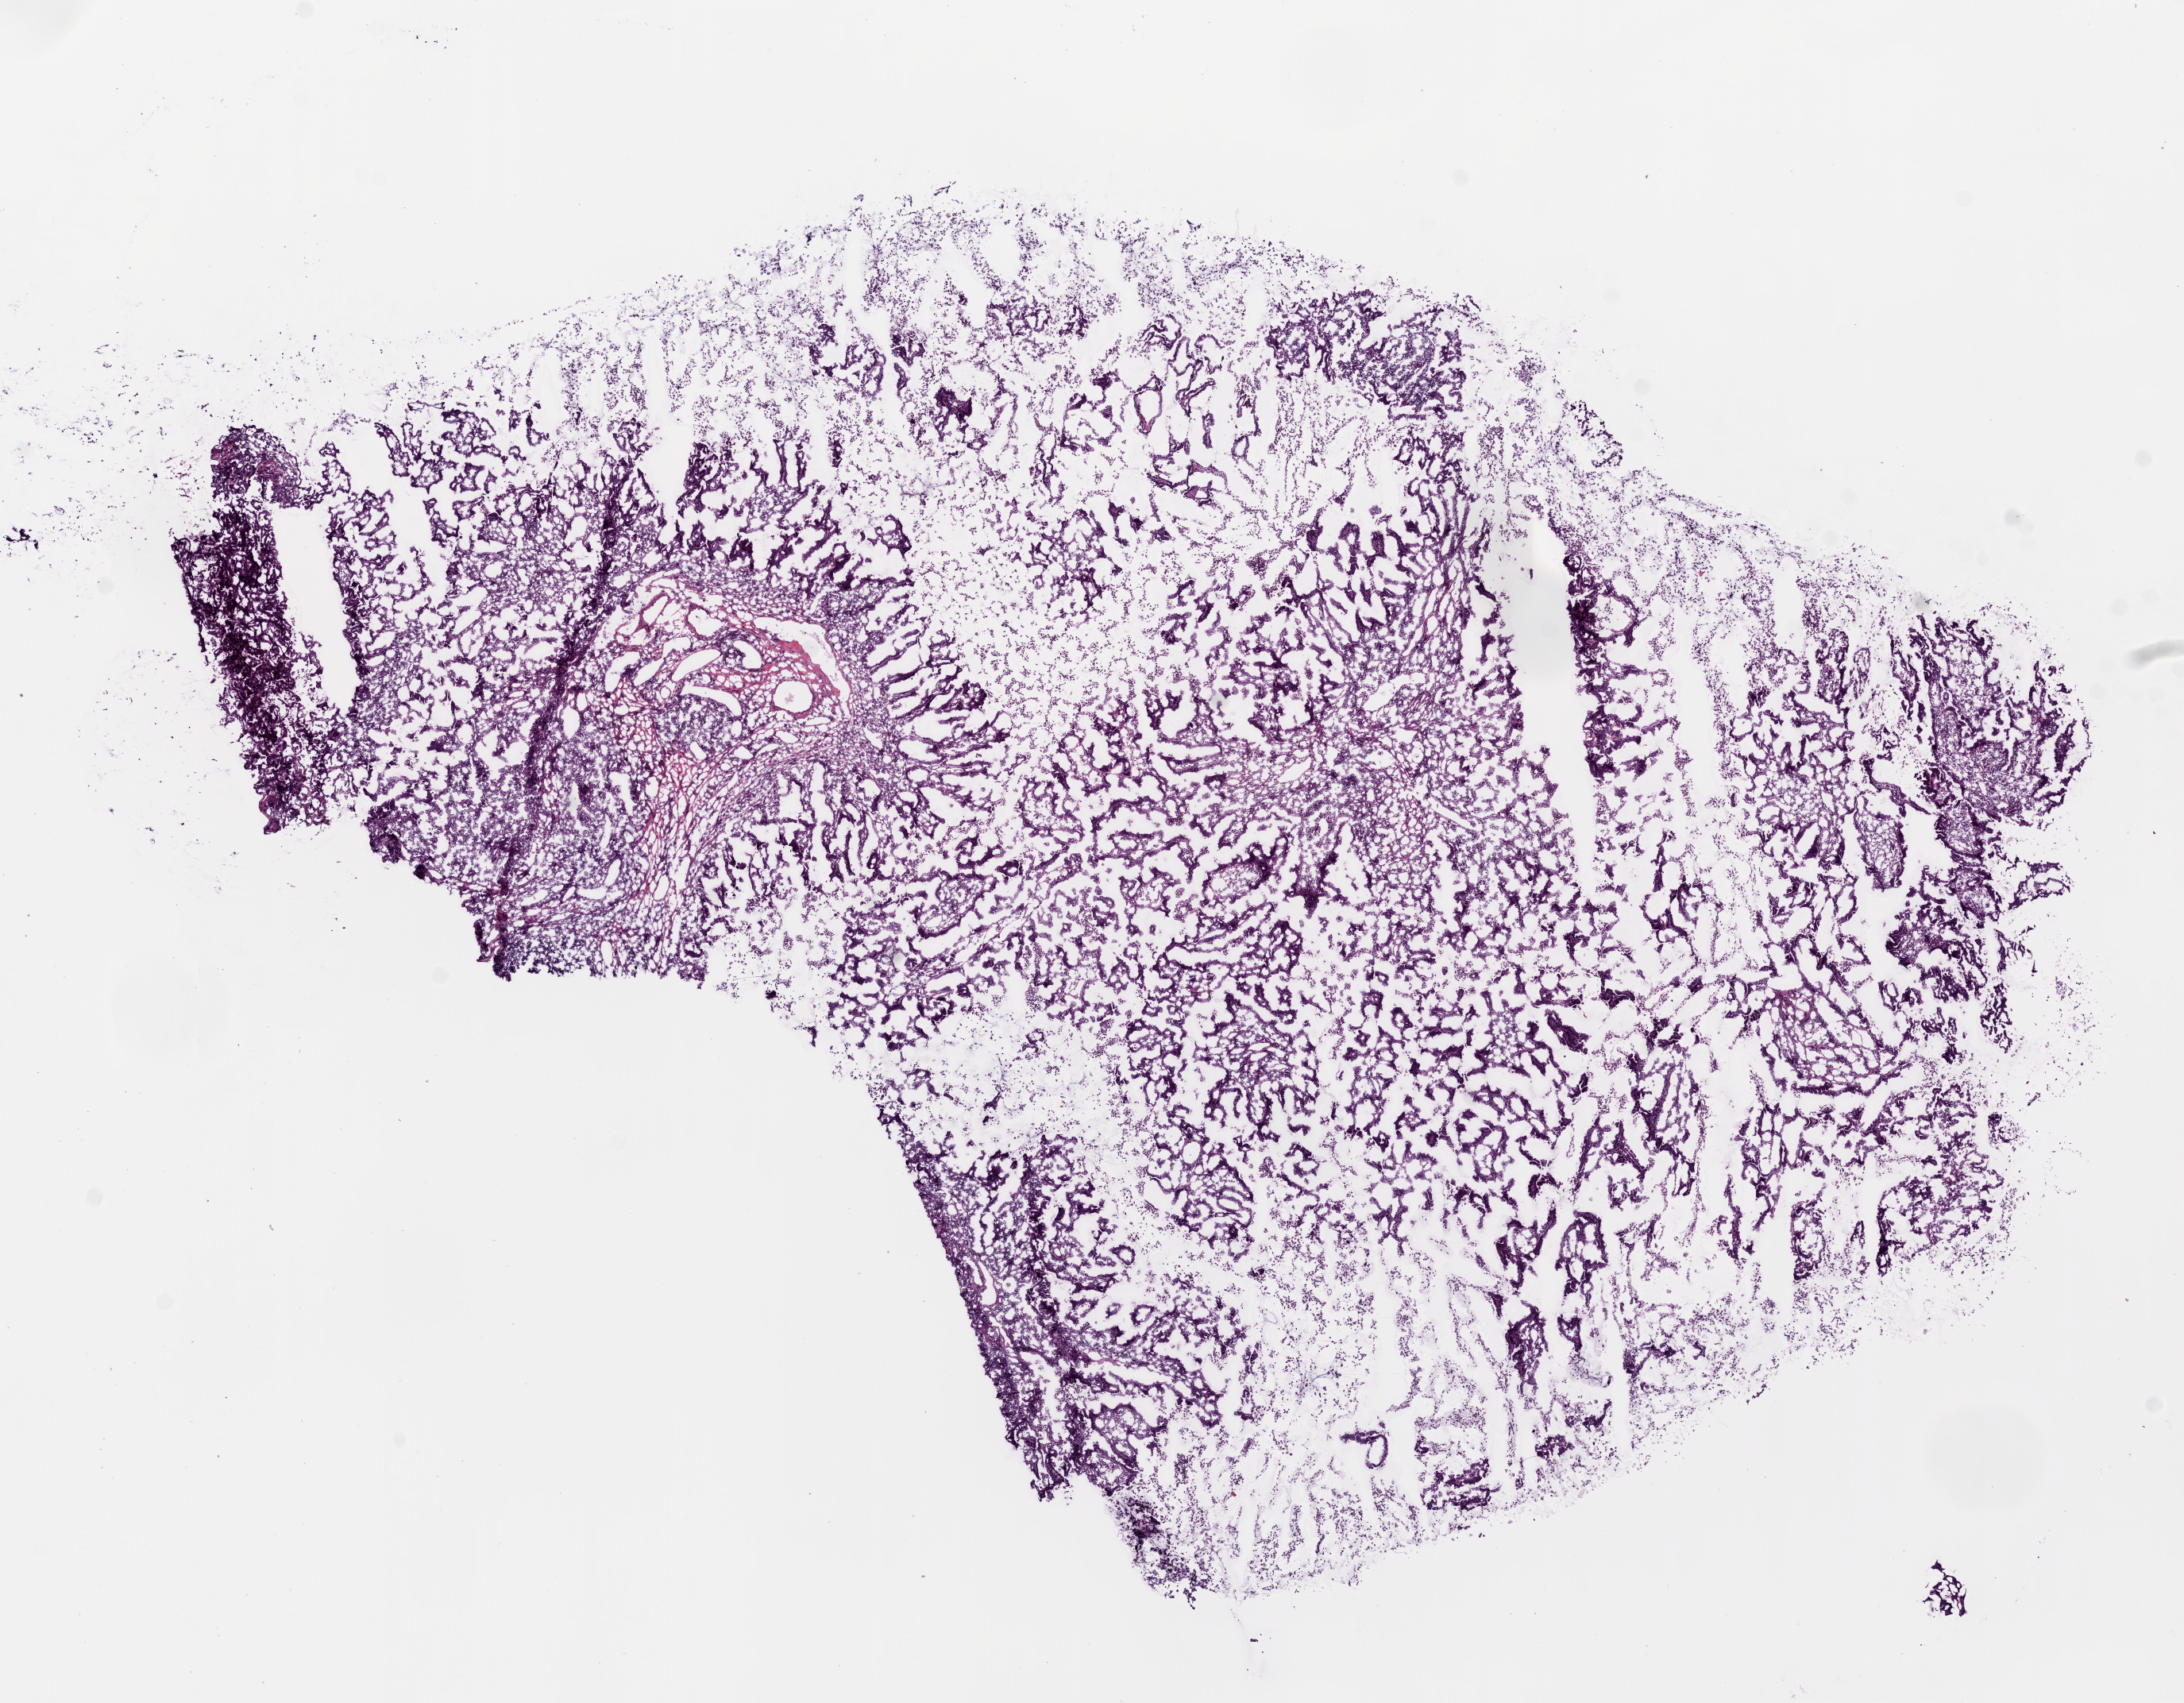
H&E-stained whole-slide image, whole scanned area (about 11.0 x 8.6 mm, slide scanned at 20x) shown as a low-resolution overview, frozen section, lung, primary tumour sample. Female patient; age at initial diagnosis 79 years. Pathologist review of this section (percent, as recorded): tumour cells 80%, tumour nuclei 50%, normal cells 15%, stromal cells 5%, necrosis 0%.
AJCC pathologic stage: IA (6th edition). Pathologic diagnosis: Papillary adenocarcinoma, NOS (upper lobe, lung).